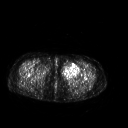
FDG PET of an extremity soft-tissue mass (from a PET/CT study), one axial slice; slice 251 of 267 in the series (ordered by position); 3.27 mm slice thickness; 128 × 128 image matrix, field of view 500 × 500 mm. Female patient, age 42 years. From the clinical record (not read from this slice): histological type: pleiomorphic leiomyosarcoma; grade: intermediate; site of the primary tumour: left thigh.
Structures marked on this image (expert contour drawn on MRI and transferred to this co-registered scan by the dataset authors):
- gross tumour volume including surrounding oedema: bounding box [x1, y1, x2, y2] px = [61, 63, 81, 79]
- gross tumour volume (mass): [61, 63, 81, 79]